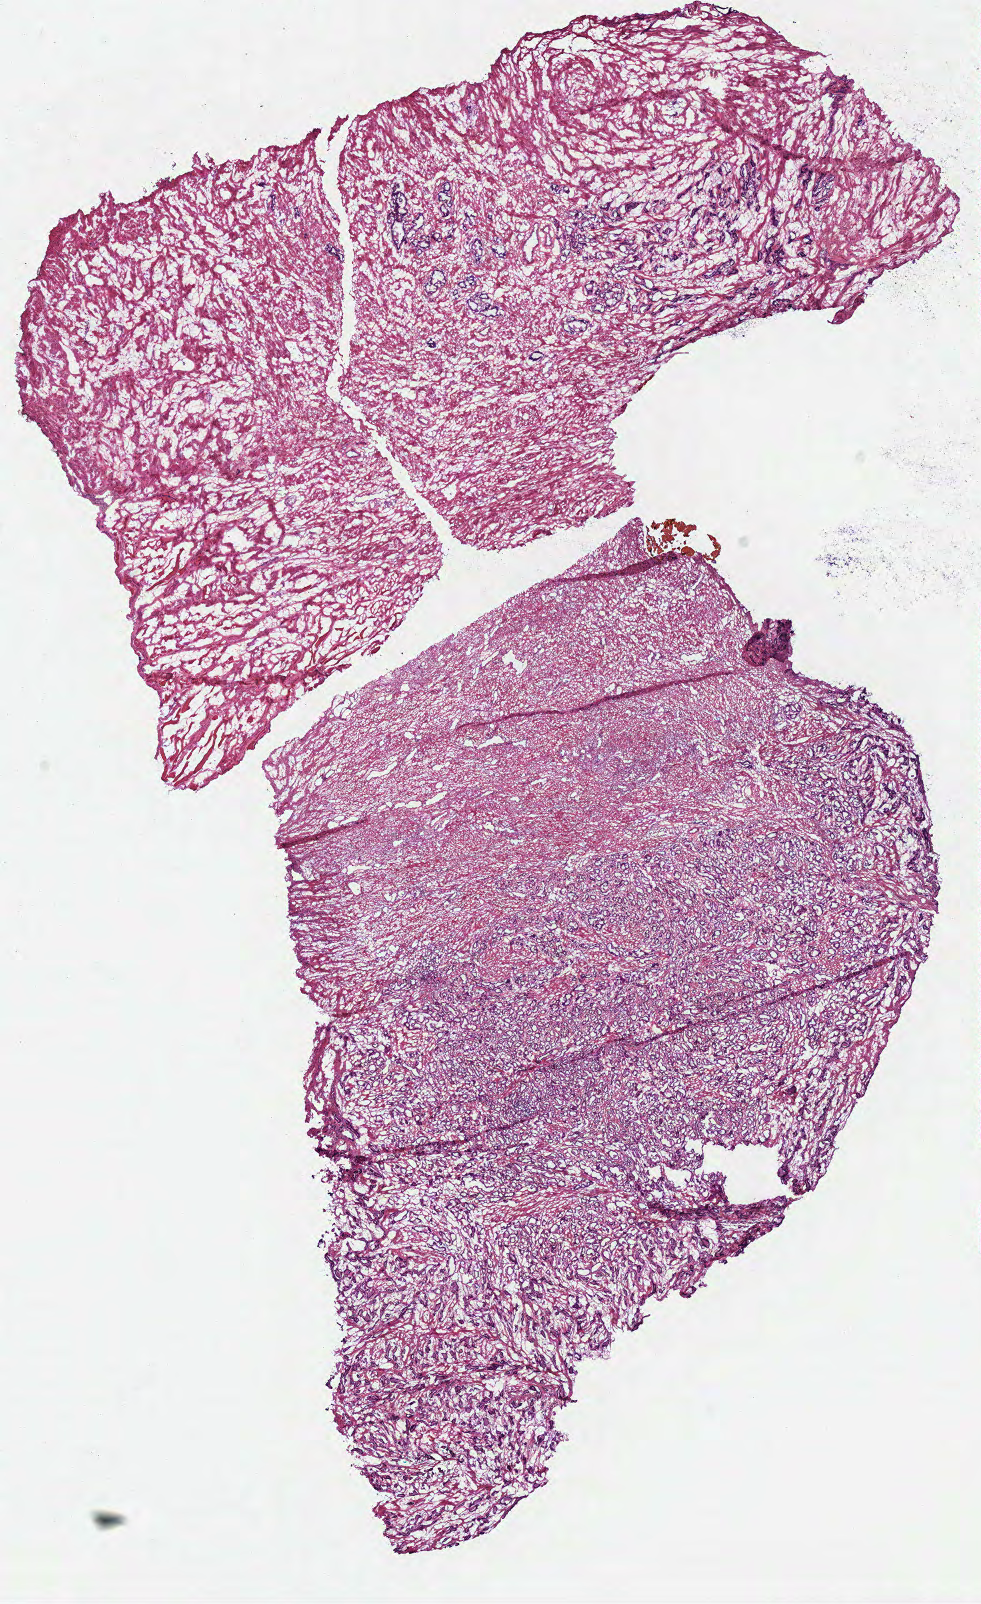
Whole-slide histology image, Hematoxylin and eosin (H&E) stained, low-resolution overview of the scanned area, about 7.7 x 12.6 mm (acquisition: 40x scan). Frozen section from the top of the tissue portion. Sample: primary tumour, prostate. Male, age 55 years at initial diagnosis. Gleason score: 7 (3+4). Composition of this section per pathologist review: tumour cells 65%, tumour nuclei 70%, normal cells 0%, stromal cells 35%, necrosis 0%.
Histologic diagnosis: Acinar cell carcinoma (prostate gland).